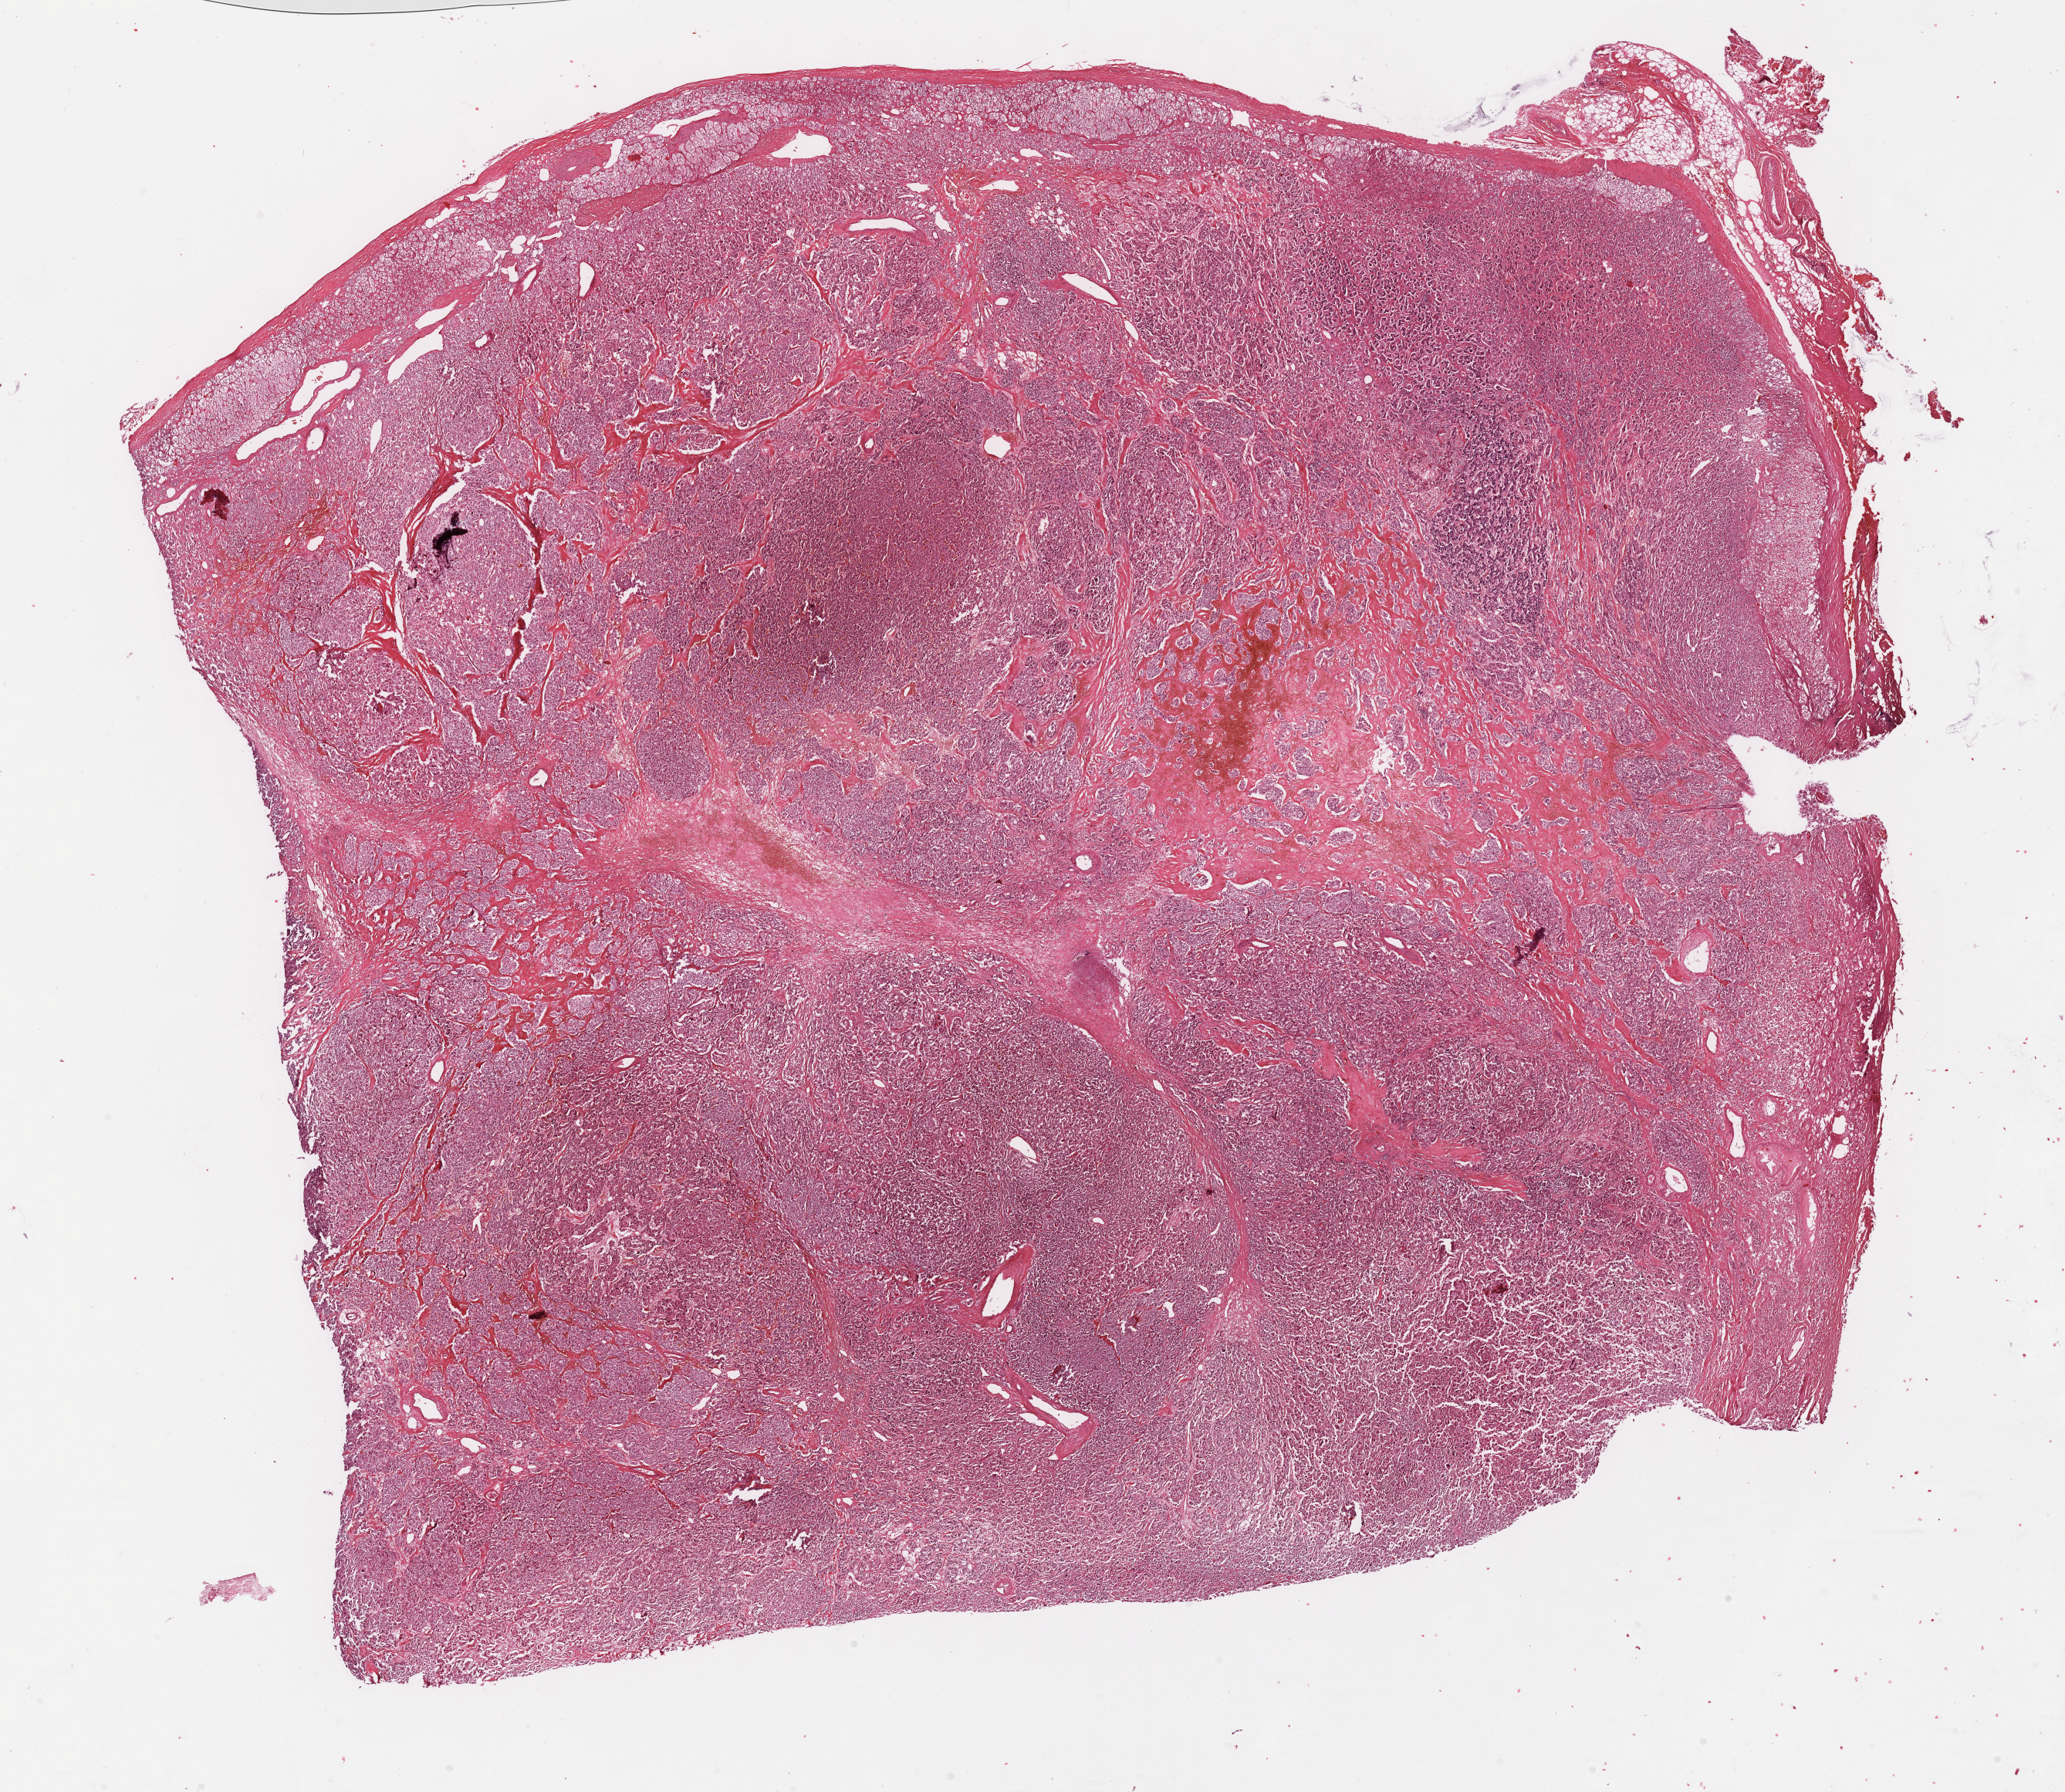
Whole-slide histology image, H&E — a low-resolution overview of the entire scanned area, about 21.6 x 18.8 mm (acquisition: 40x scan). FFPE section. Sample: primary tumour, adrenal gland. Male, age 76 years at initial diagnosis.
* diagnosis: Pheochromocytoma, malignant